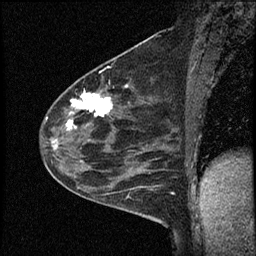
Breast MRI (dynamic contrast-enhanced), one sagittal slice. Position 39 of 60 along the scan axis. Dynamic contrast-enhanced study with each time point stored as its own series, time point 2 of 4 at this slice position (early post-contrast, ordered by acquisition time). 1.5 T. TE 4.2 ms, TR 17.6 ms. 256 × 256 image matrix. Patient: female, 53 years. Case-level facts recorded for this patient, not image findings: setting: breast cancer imaged before/during neoadjuvant chemotherapy; receptor status: HR-positive, HER2-negative.
Outlined on this slice (semi-automatically segmented with operator editing):
- analysis volume of interest (the breast-tissue region the enhancement analysis was run in; not a lesion): bounding box (x1, y1, x2, y2) in pixels: (42, 69, 156, 199)
- tumour enhancement mask (voxels above the 100 % enhancement threshold inside the analysis volume of interest): (53, 85, 128, 162)